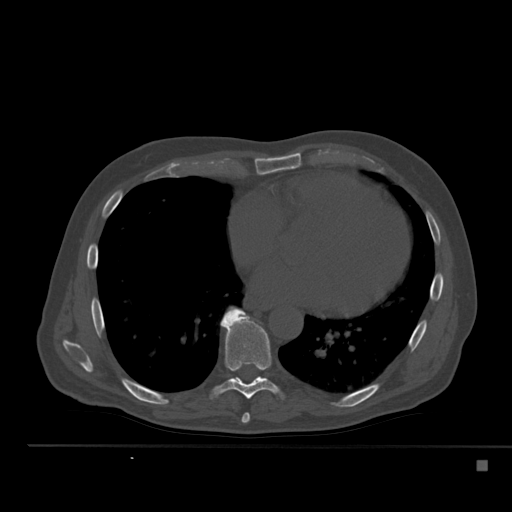
CT including the spine, one axial slice; slice 307 of 517 in the series (ordered by position); bone window (W 1800 / L 400 HU); 1.5 mm slice thickness; 512 × 512 image matrix, field of view 408 × 408 mm. Male patient, age 70 years. From the clinical record (not read from this slice): primary cancer: renal; vertebrae with lytic lesions (as recorded): T4, T6, T10, T12, L3, L4, L5.
Outlined on this slice (semi-automatically segmented with operator editing):
- T7 vertebra: bounding box <241,413,250,423> (left, top, right, bottom; pixels)
- T8 vertebra: <212,307,283,399>